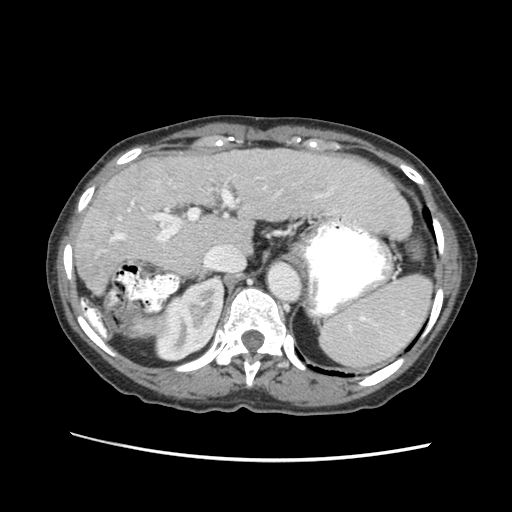
Contrast-enhanced abdominal CT (liver protocol), one axial slice. Position 39 of 63 along the scan axis. Reconstruction kernel STANDARD. 120 kVp. Soft-tissue window (W 400 / L 40 HU). 512 × 512 image matrix. Case-level facts recorded for this patient, not image findings: diagnosis: hepatocellular carcinoma (patient treated with transarterial chemoembolisation; whether this scan precedes or follows treatment is not stated here); TNM stage (as recorded): Stage-I; Child-Pugh class: B; tumour nodularity: uninodular.
Annotated regions visible in this slice (semi-automatic segmentation, software-assisted and operator-edited):
- abdominal aorta: box from (x=268, y=262) to (x=299, y=299) px
- liver parenchyma outside the tumour (the mass and vessels are separate outlines, so this box may not span the whole liver): (x=74, y=145)–(x=410, y=274)
- liver vessels: (x=110, y=183)–(x=329, y=241)